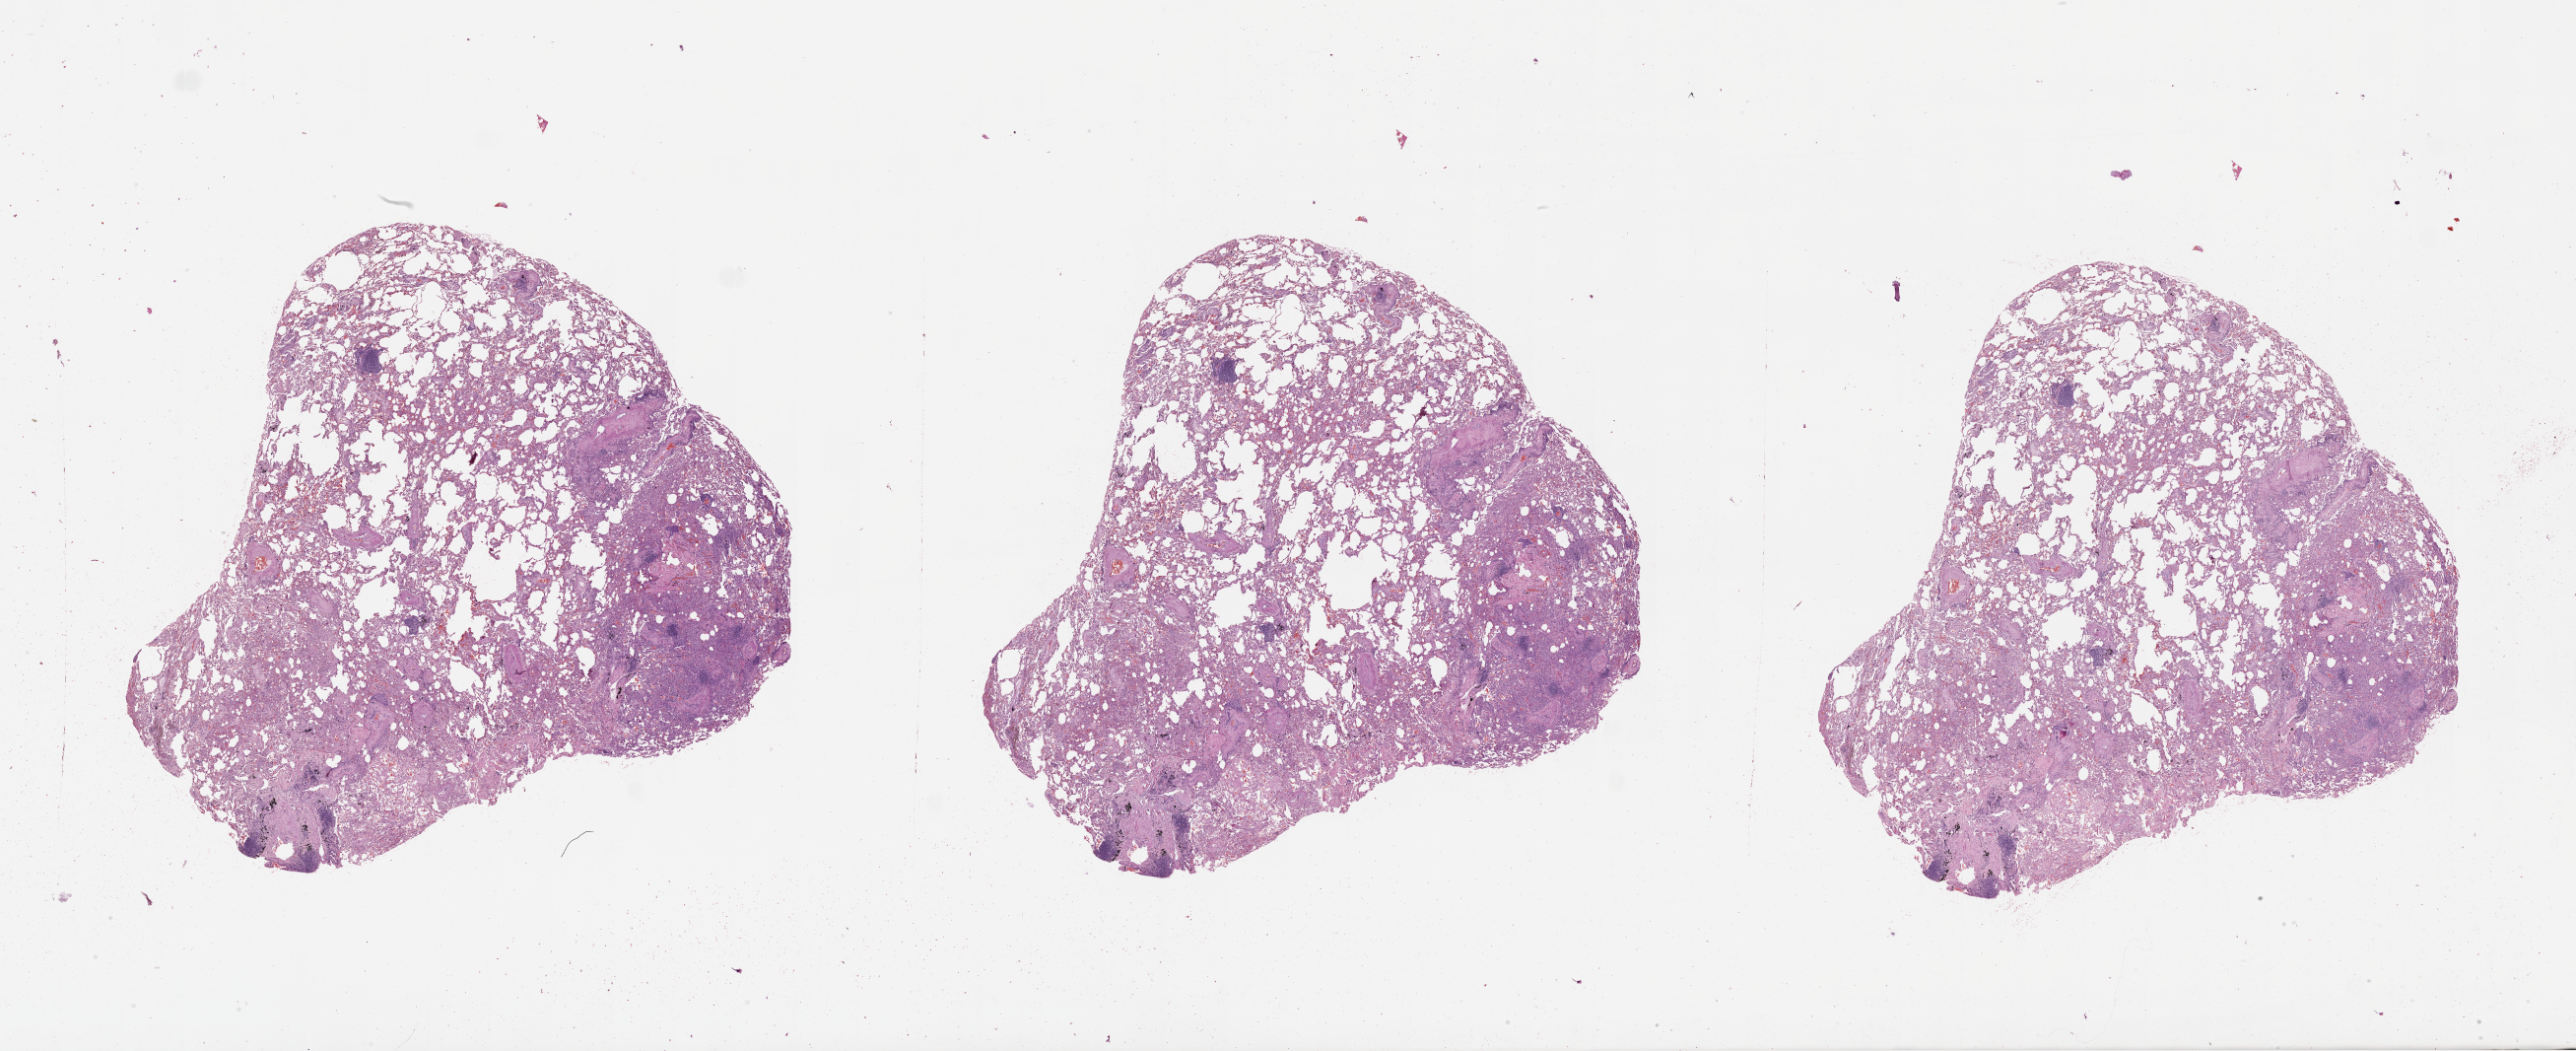
H&E-stained whole-slide image — low-resolution overview of the scanned area, about 42.1 x 17.2 mm, lung, normal (non-tumour) tissue. 74-year-old male patient.
- this section: normal (non-tumour) tissue from the same patient
- patient diagnosis (cohort enrolment): squamous cell carcinoma (lung)